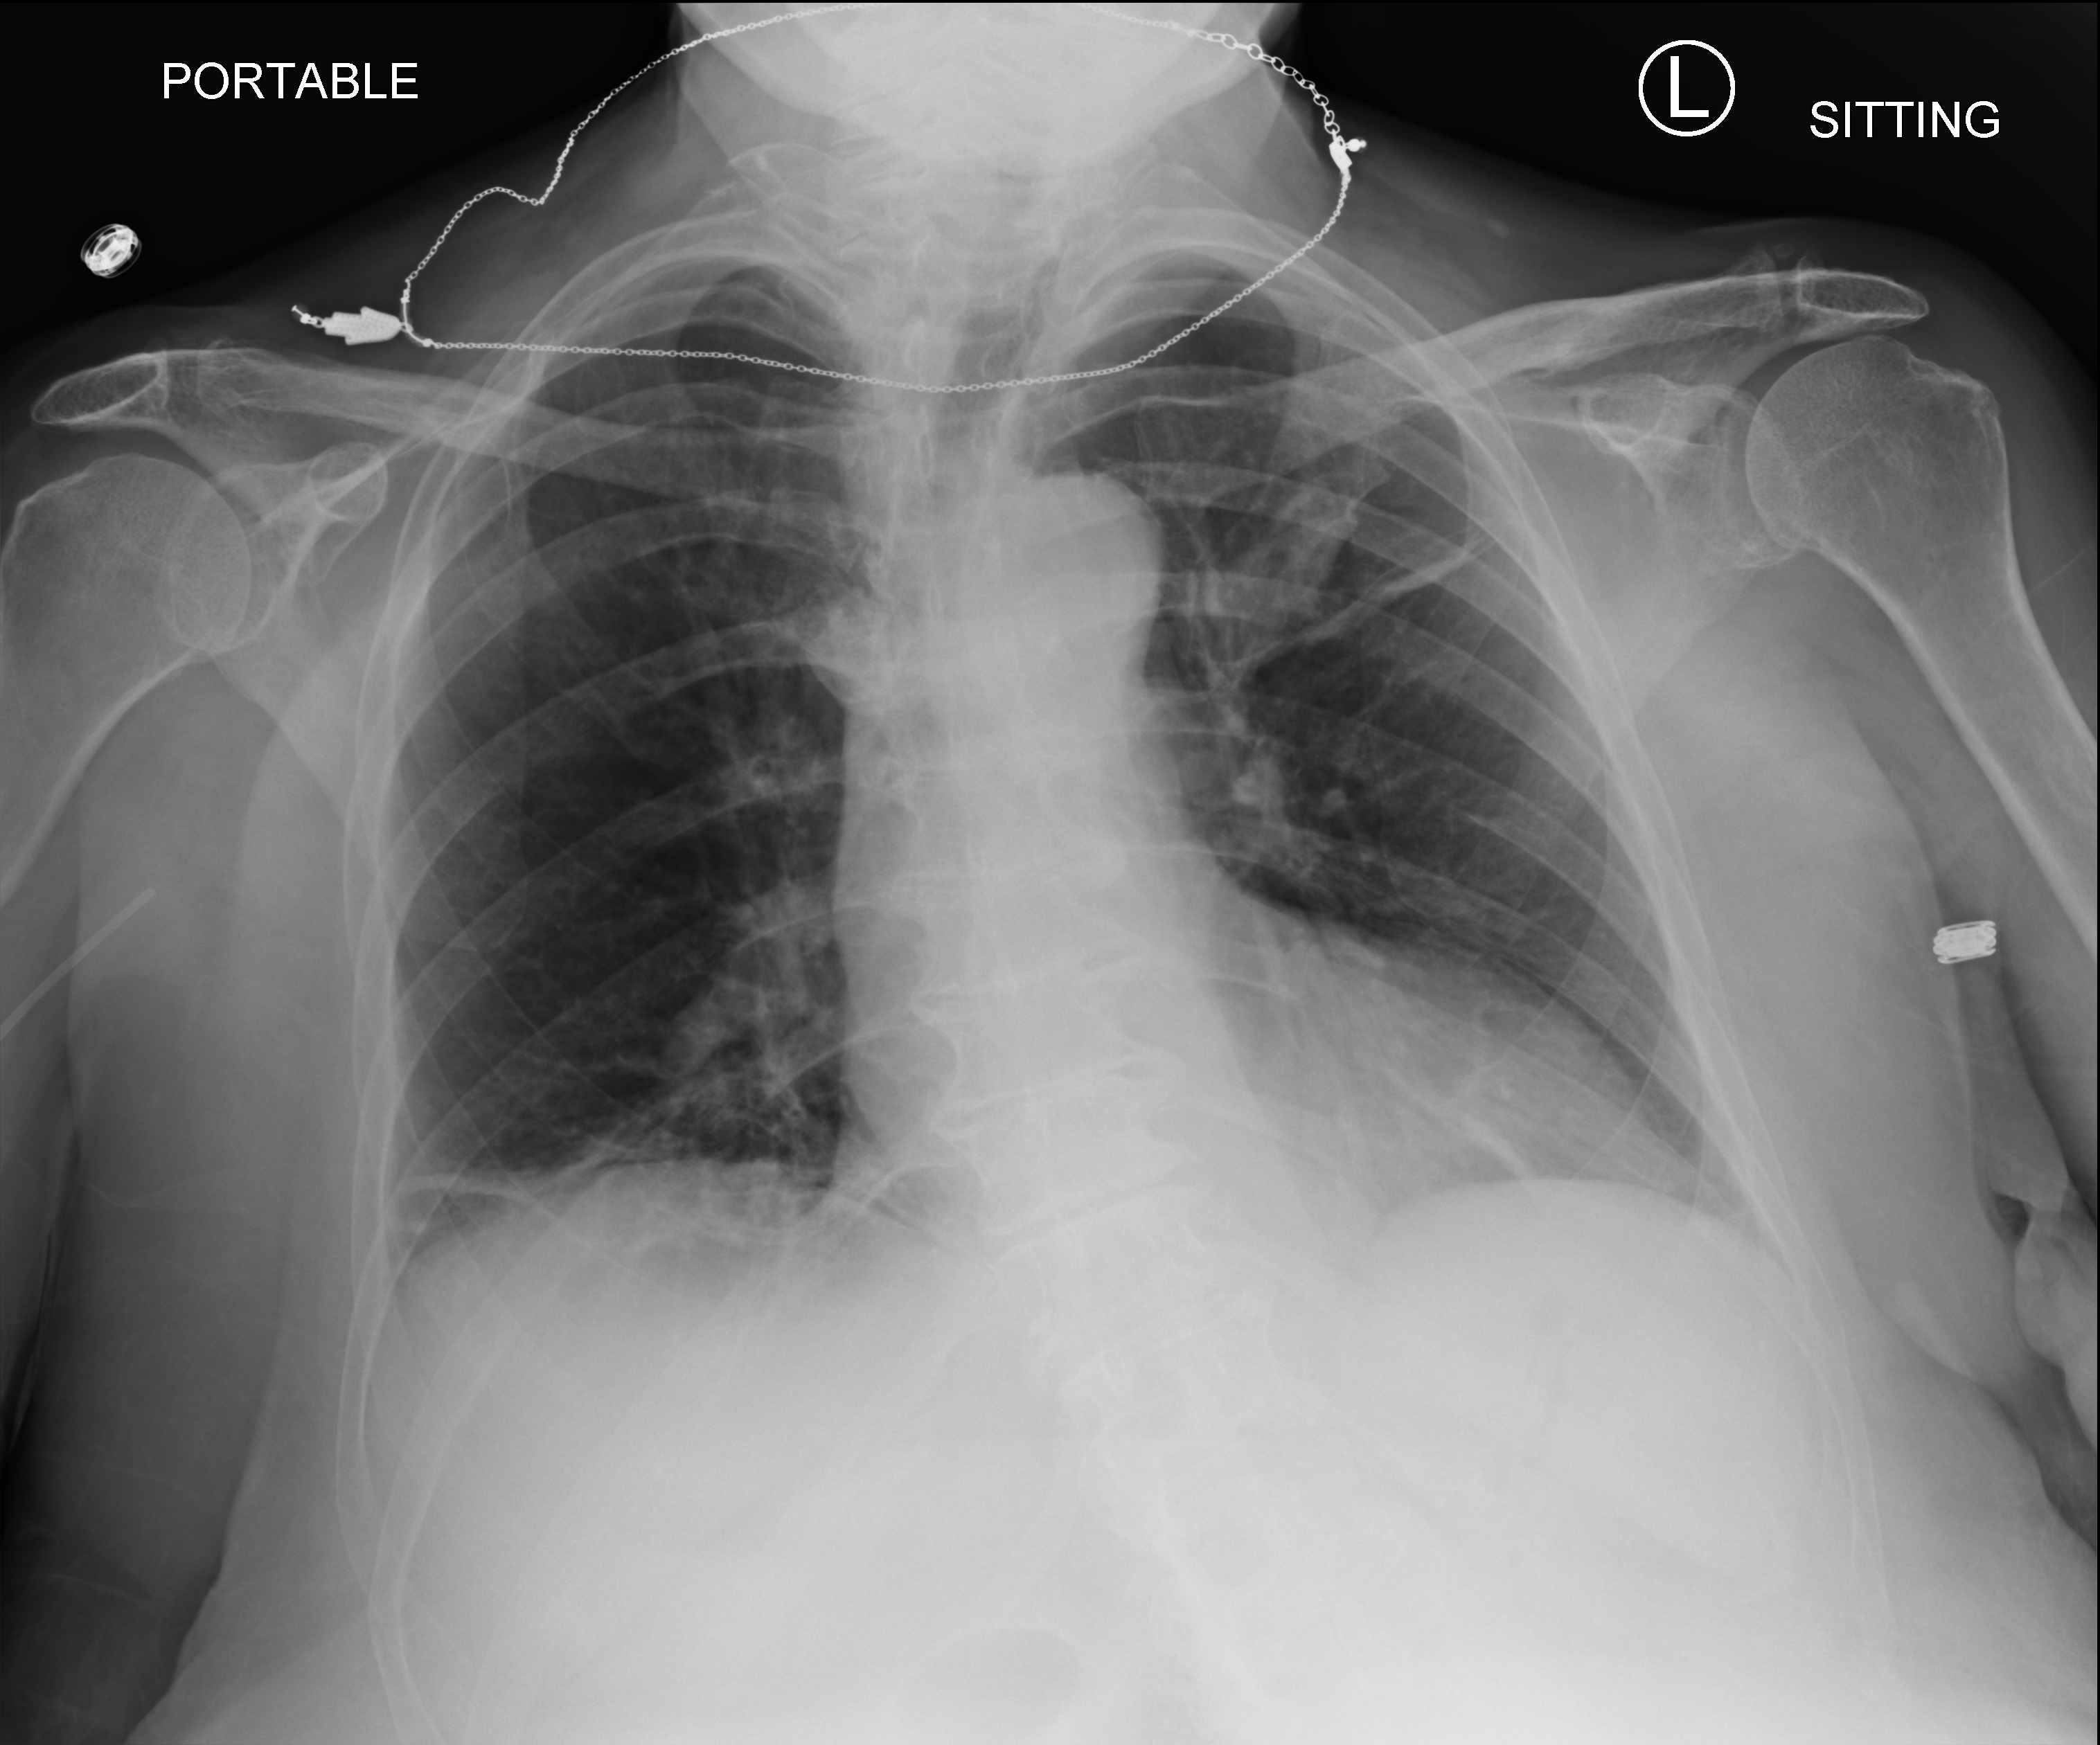
Bedside chest radiograph (computed radiography), anteroposterior (AP) projection. Patient hospitalised with COVID-19; female, aged 60–74 years.
From the hospital-stay record, not from the radiograph (when in the stay this image was taken is not recorded):
- mechanically ventilated during this hospital stay: no
- admitted to intensive care during this hospital stay: yes